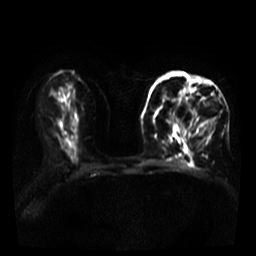
Breast MRI, one axial slice. Diffusion-weighted series; image 2 of 4 stored at this slice position (different b-values; order by instance number). 3 T. 5 mm slice thickness. 256 × 256 image matrix, field of view 320 × 320 mm. Female patient.
Outlined on this slice (outlined manually by an expert reader):
- tumour on diffusion-weighted imaging: bounding box [x1, y1, x2, y2] px = [158, 84, 195, 110]